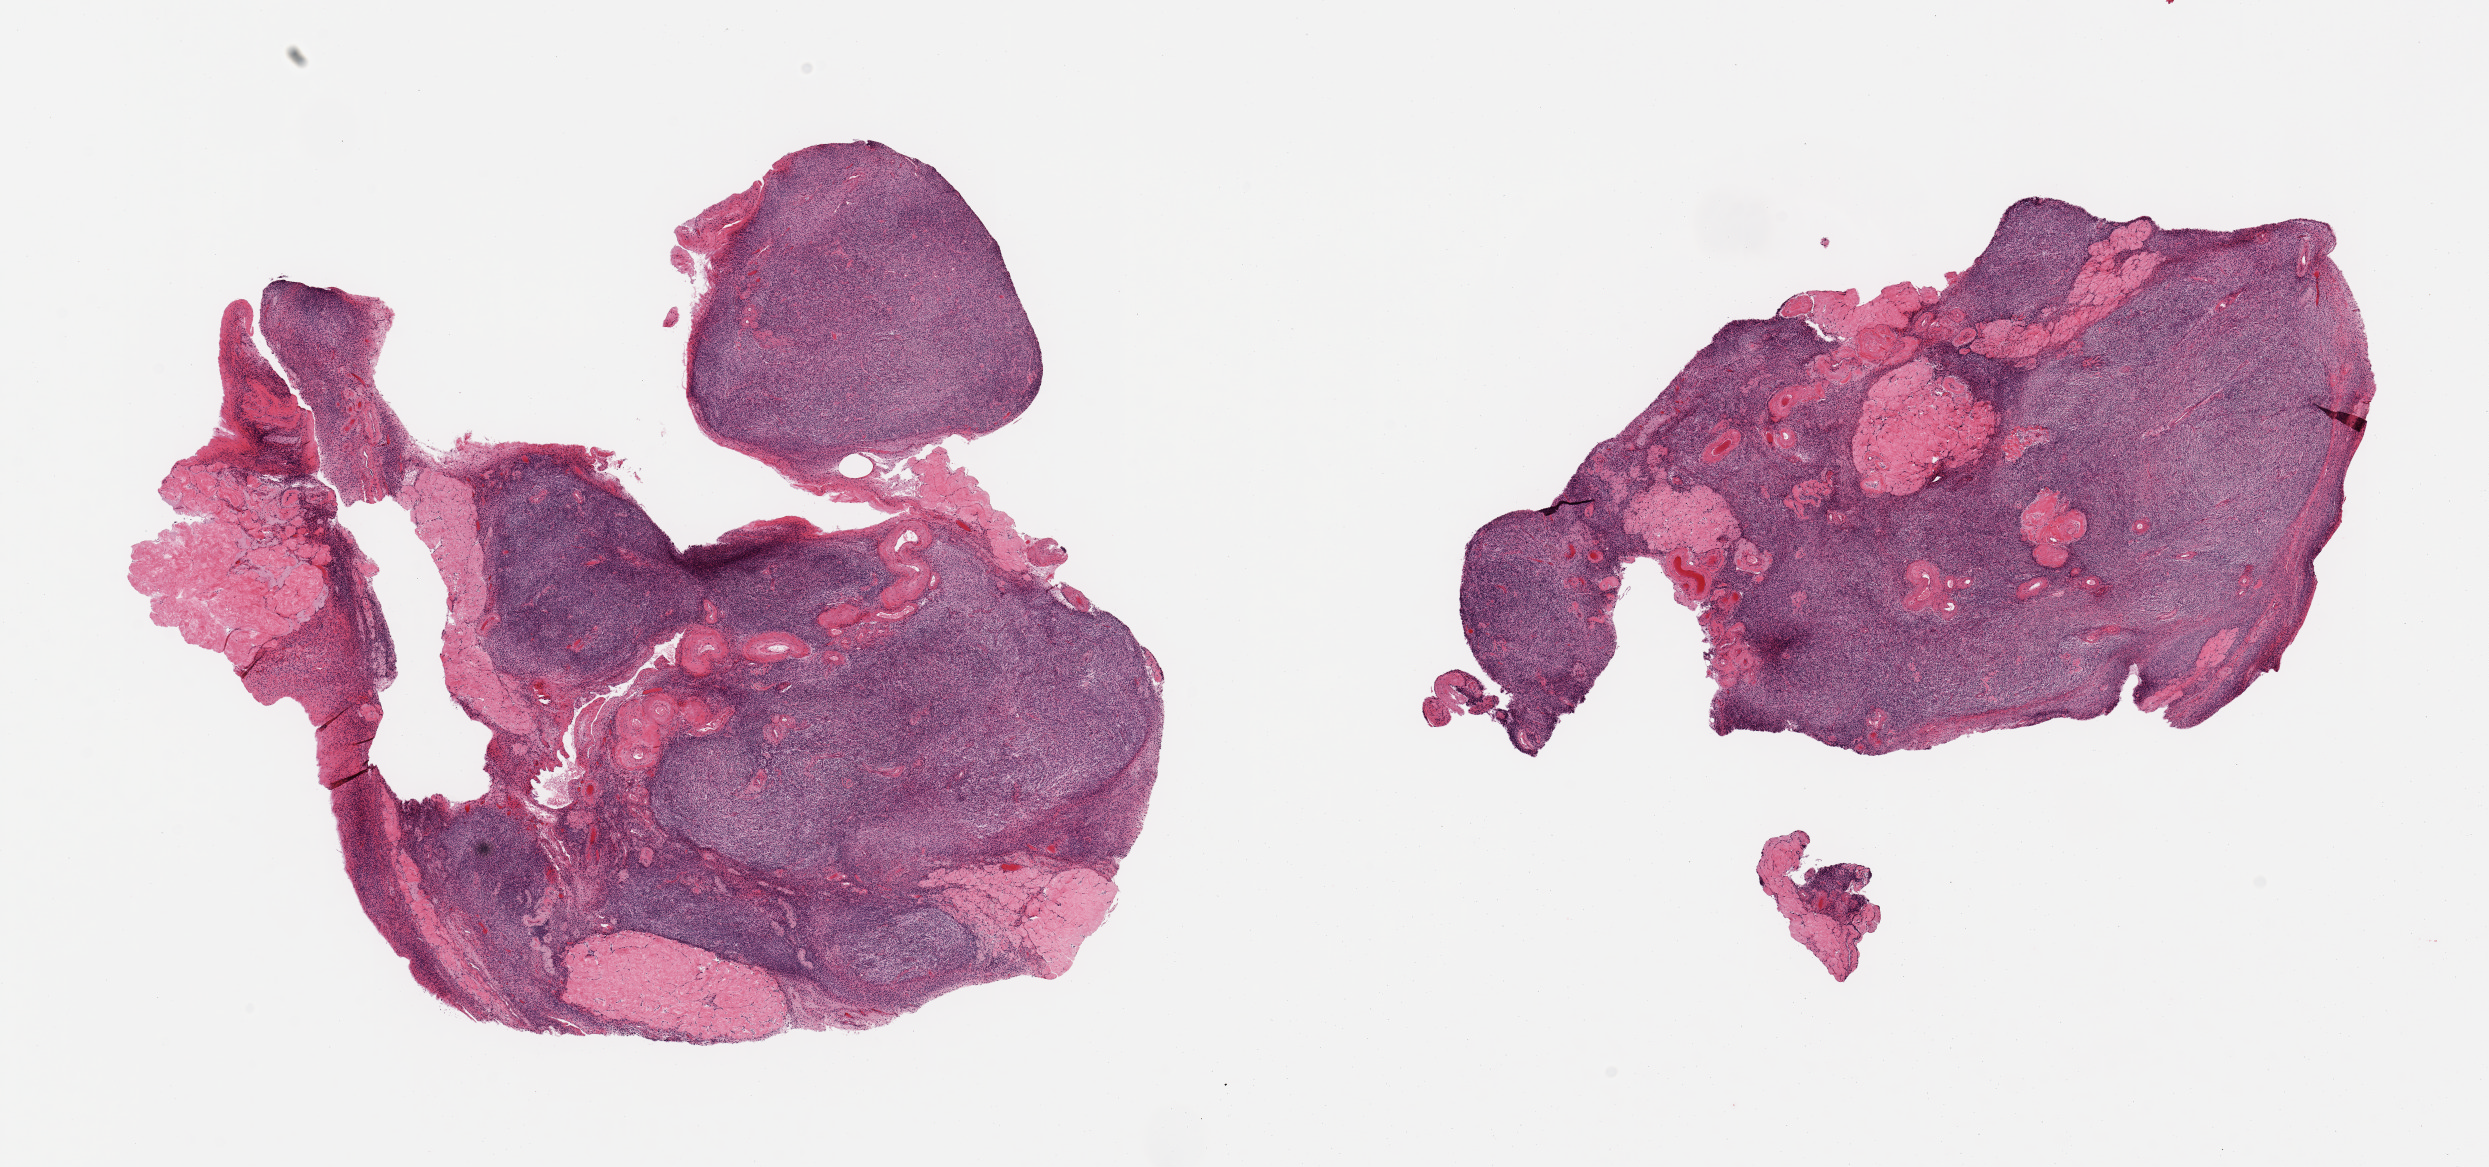
Whole-slide image, haematoxylin and eosin stain, whole scanned area (about 19.7 x 9.2 mm) shown as a low-resolution overview, PAXgene-fixed, paraffin-embedded tissue, target tissue: ovary, tissue donor sample. Donor: female.
Review note (as recorded): 2 pieces; atrophic; corpora albicantia comprise 20 & 10%.